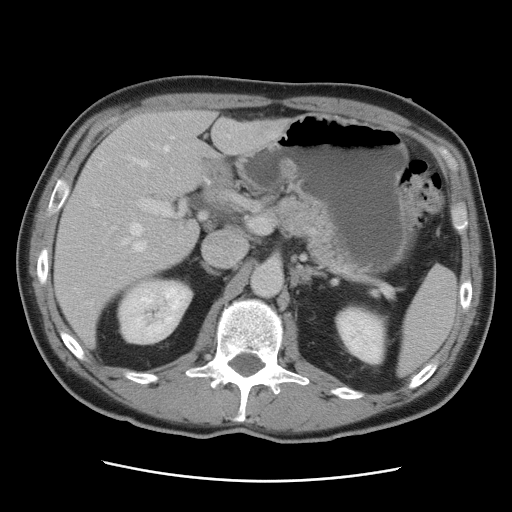
Contrast-enhanced abdominal CT, one axial slice; position 52 of 89 along the scan axis; 120 kVp; intravenous contrast given; soft-tissue window (W 400 / L 40 HU); 512 × 512 image matrix, field of view 366 × 366 mm. Male patient, age 59 years. Case-level facts recorded for this patient, not image findings: diagnosis: colorectal cancer liver metastases, imaged before liver resection; multiple liver metastases: yes; largest metastasis: 0.6 cm; chemotherapy before resection: no.
Annotated regions visible in this slice (outlined manually by an expert reader):
- hepatic veins: bounding box <78,135,238,305> (left, top, right, bottom; pixels)
- liver: <54,111,291,349>
- planned liver remnant (the part of the liver to remain after resection): <71,111,220,241>
- portal vein (with intrahepatic branches): <140,199,263,240>